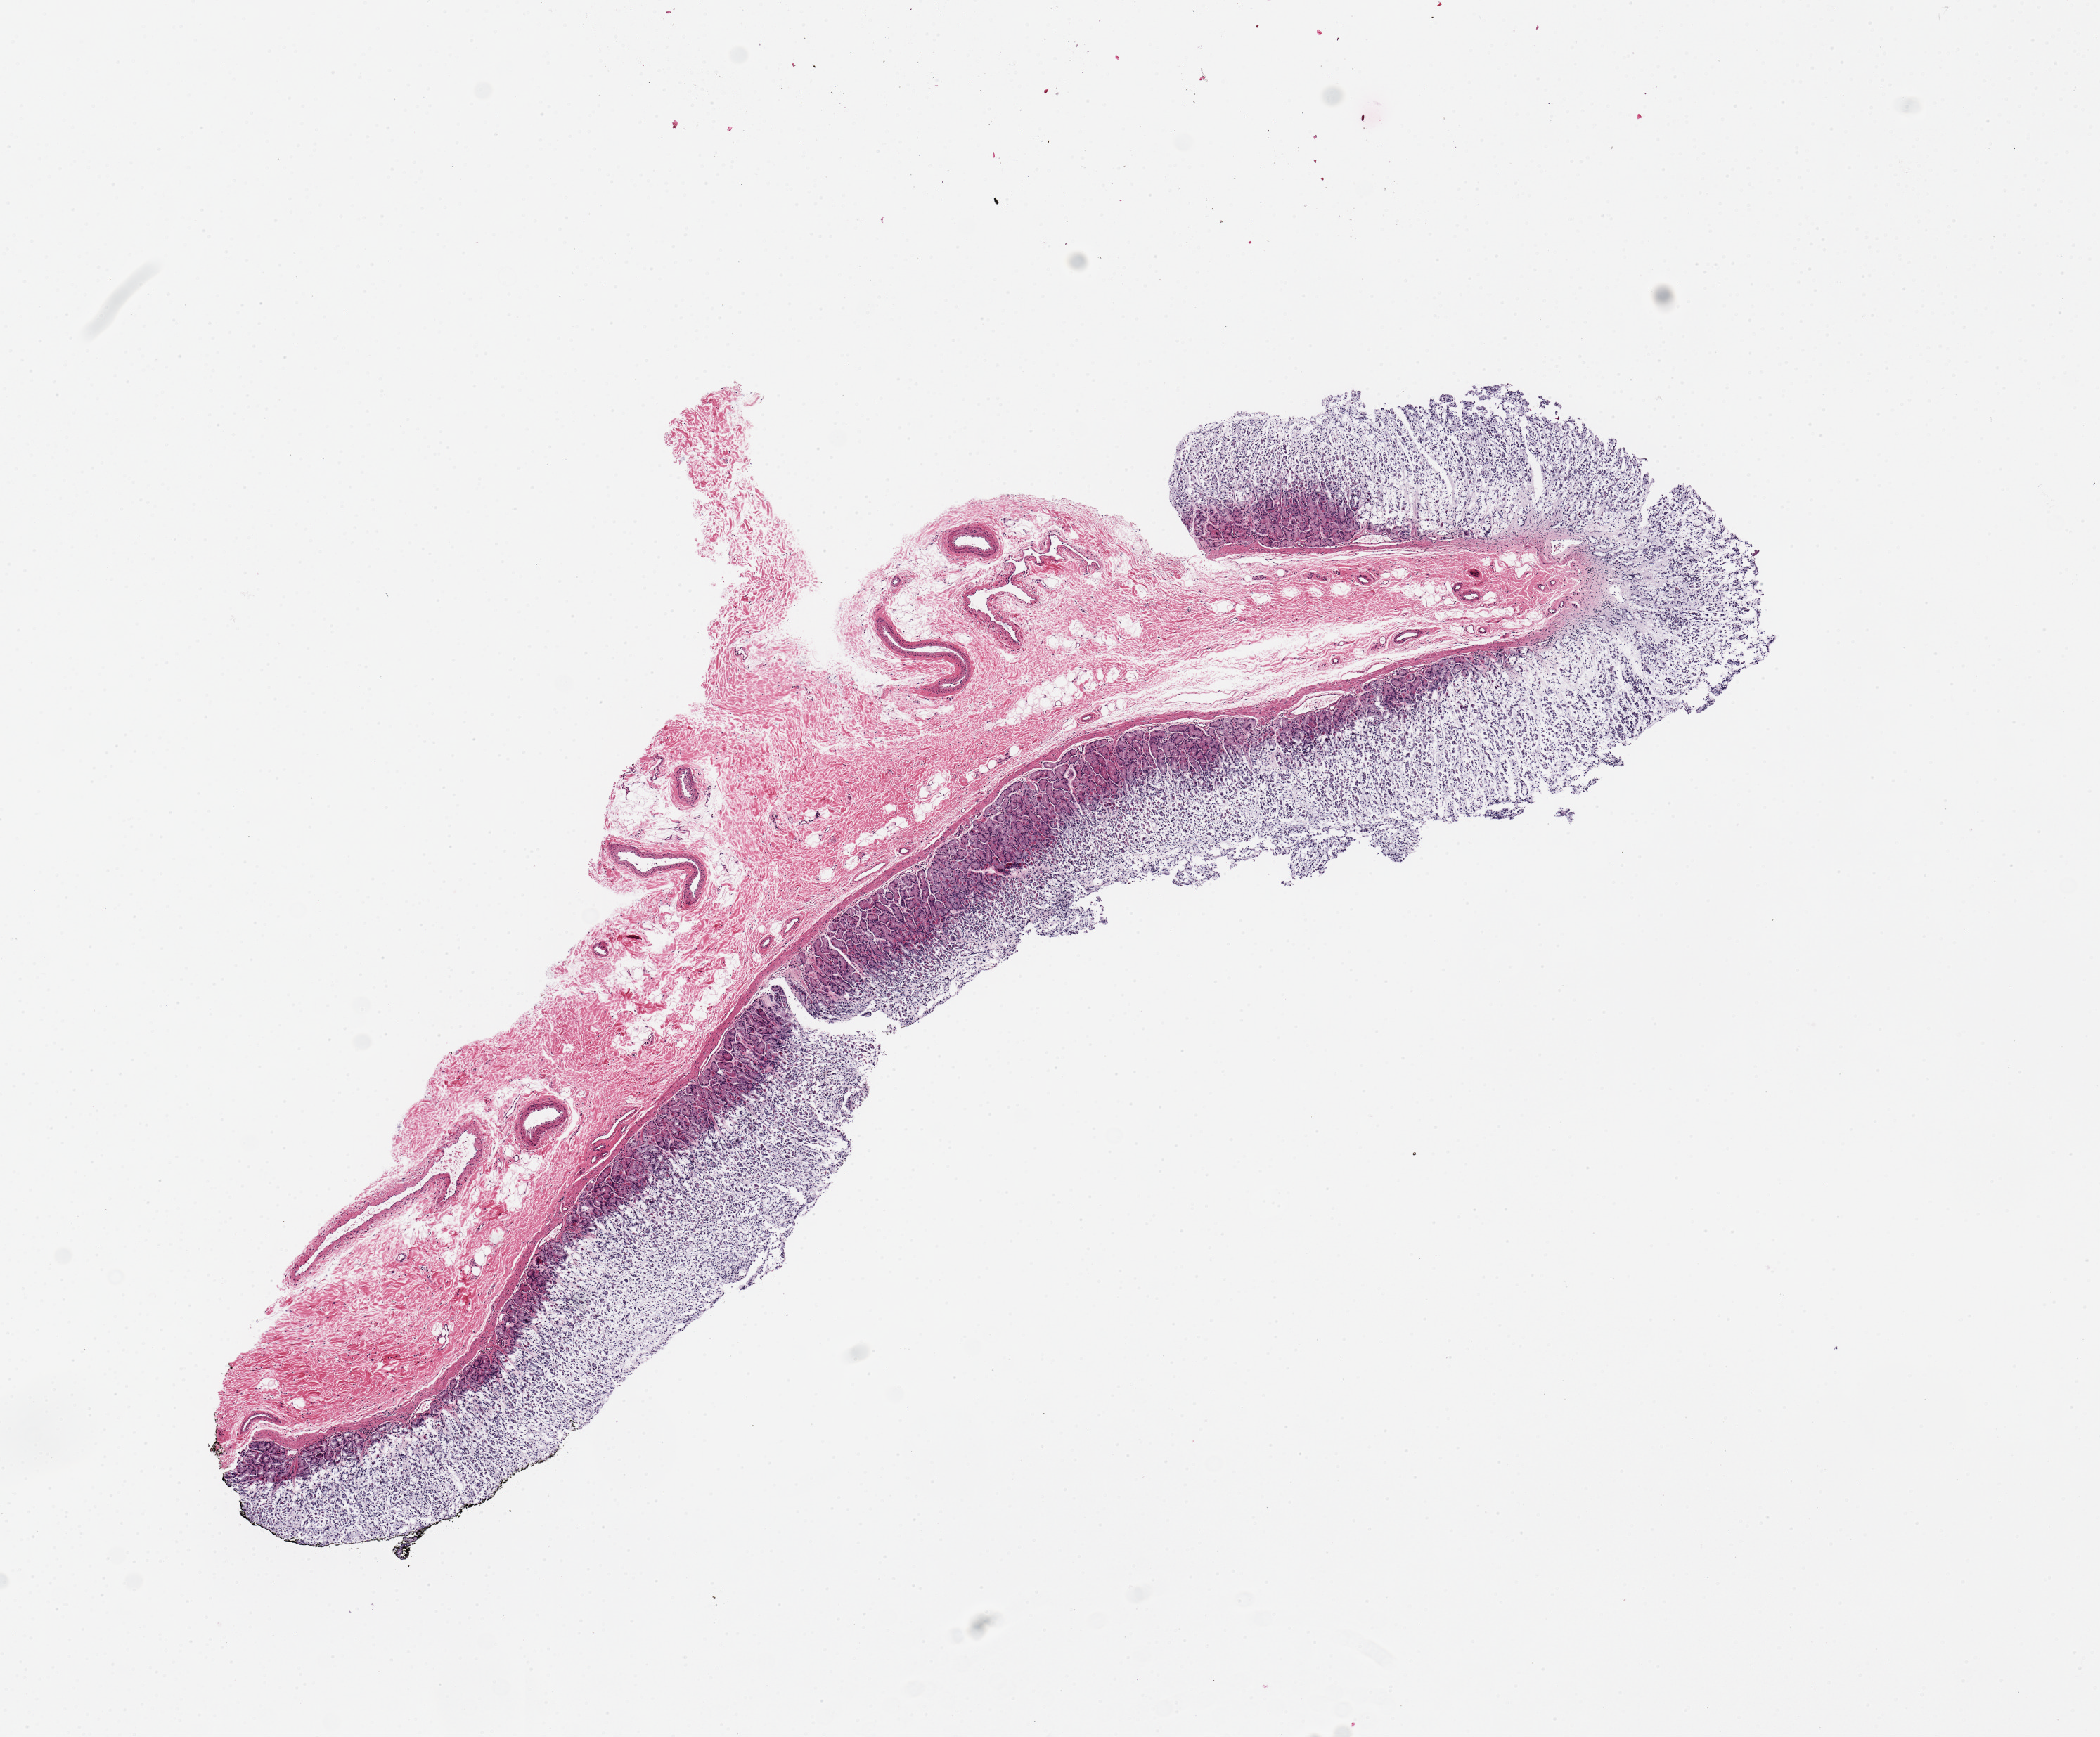
Haematoxylin and eosin whole-slide image — whole scanned area (about 11.8 x 9.8 mm) shown as a low-resolution overview. PAXgene-fixed, paraffin-embedded tissue. Target tissue: stomach. Donor tissue sample. Donor sex: male.
Pathologist's review note for this sample: 1 piece; comparable to 25 block.